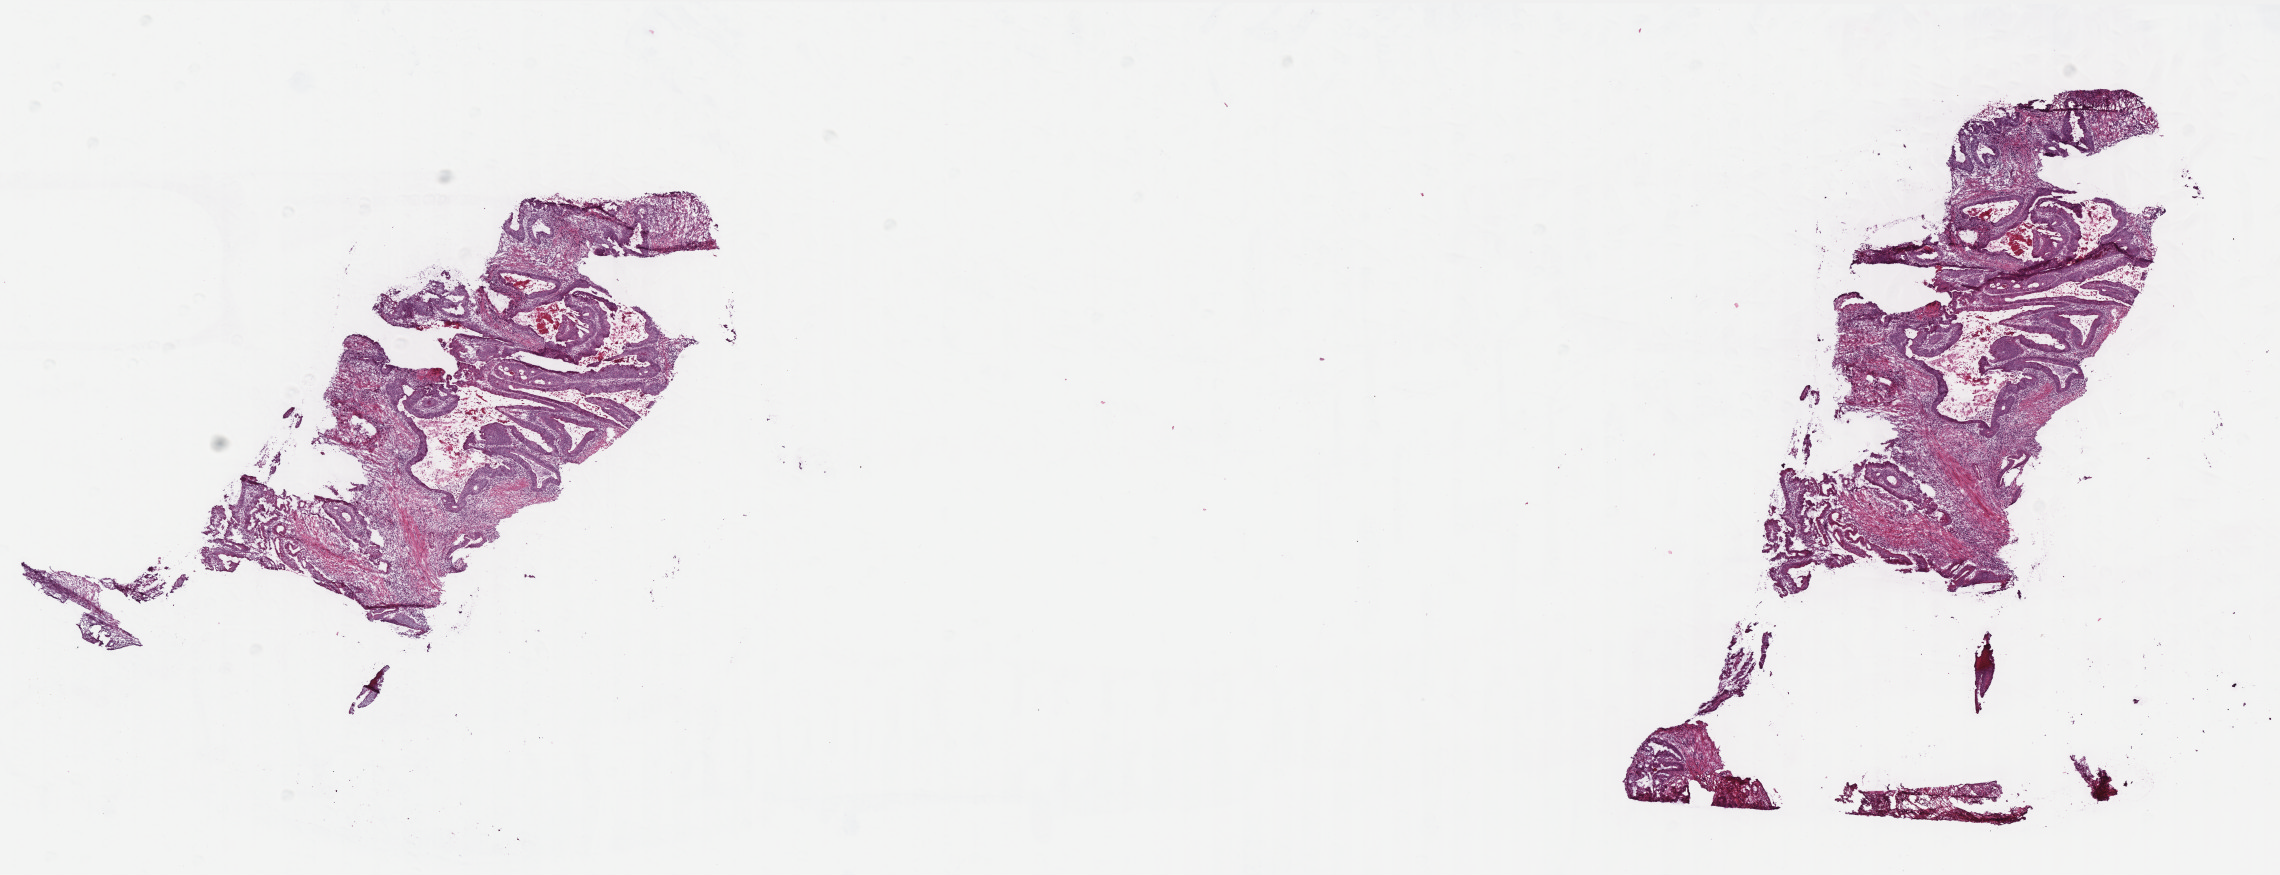
Digitized H&E tissue section (whole slide) — shown as a low-resolution overview of the whole scanned area (about 18.3 x 7.0 mm, slide scanned at 40x); frozen section; colon, primary tumour sample. Male patient; age at initial diagnosis 76 years. Composition of this section per pathologist review: tumour cells 70%, tumour nuclei 60%, normal cells 0%, stromal cells 28%, necrosis 2%. Infiltration values recorded for this section: lymphocyte infiltration 17%, monocyte infiltration 5%, neutrophil infiltration 10%.
AJCC pathologic stage: I. Pathologic diagnosis: Adenocarcinoma, NOS (sigmoid colon). Lymph nodes positive (case pathology): 0 of 36 examined.